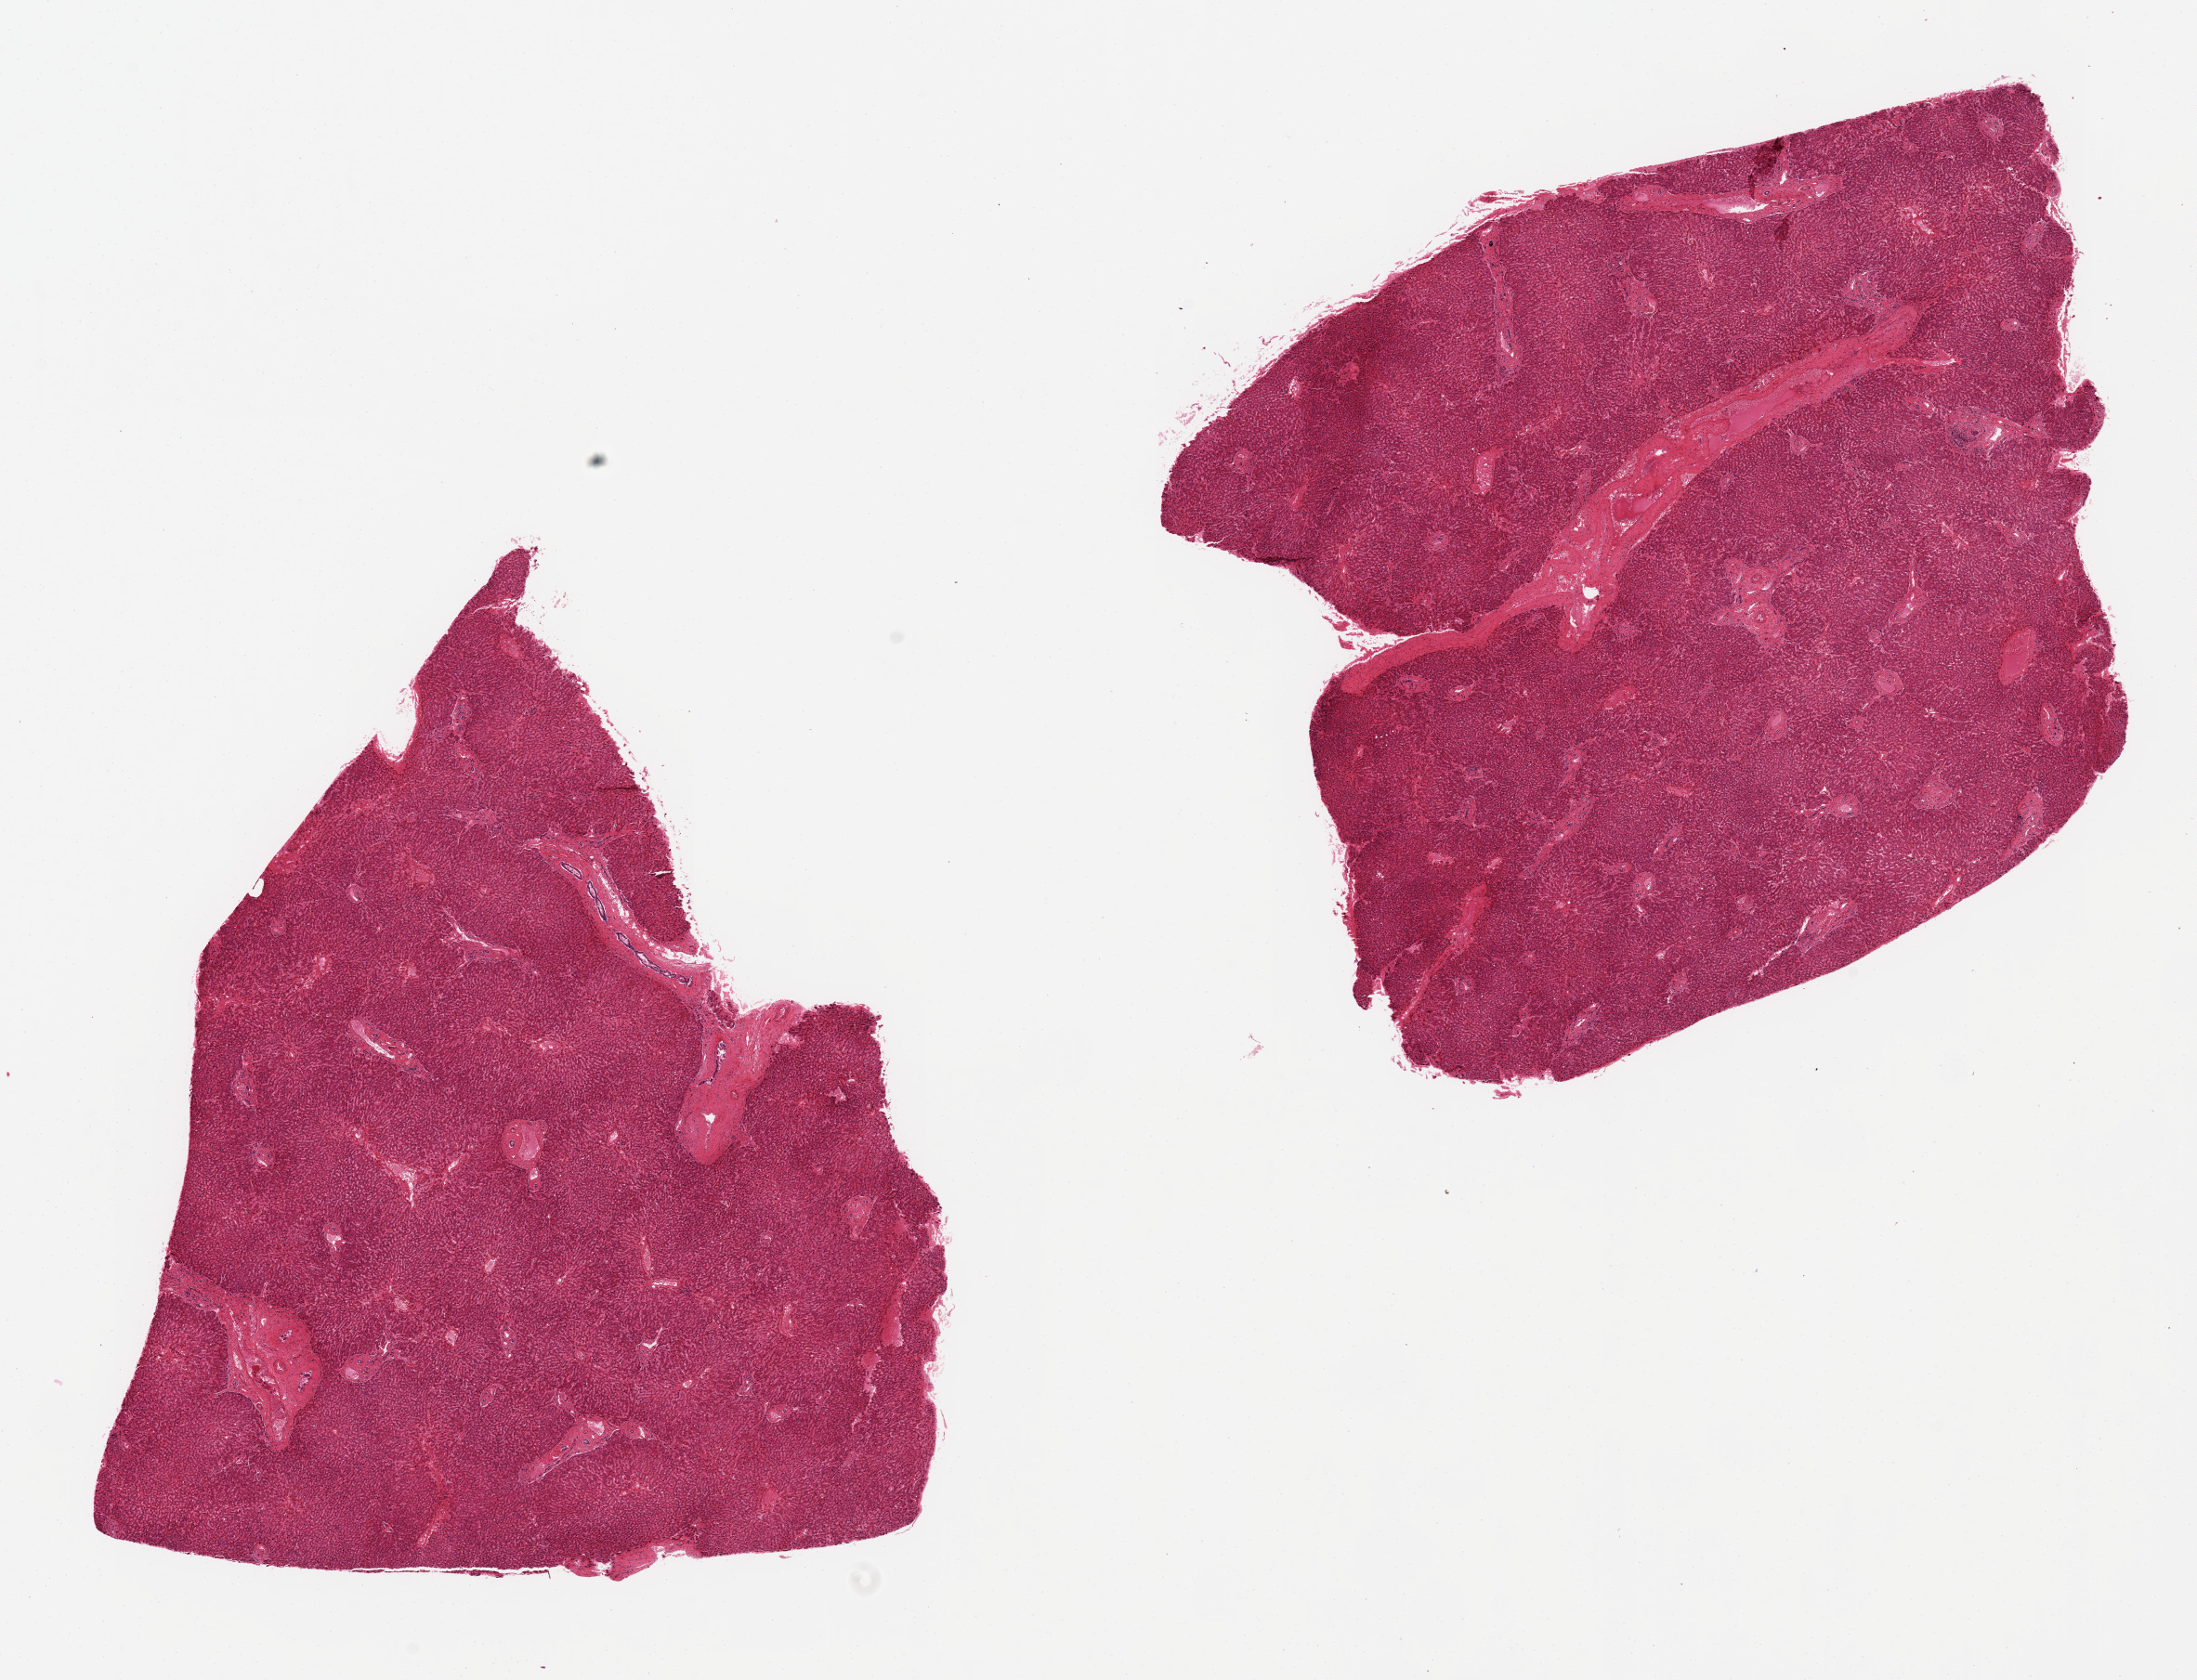
Digitized H&E-stained section, brightfield — shown as a low-resolution overview of the whole scanned area (about 18.7 x 14.3 mm, acquisition: 20x scan). PAXgene-fixed, paraffin-embedded tissue. Target tissue: liver. Donor tissue sample. Female donor.
Pathologist's review note for this sample: 2 pieces, 9x7 & 7x7 mm.